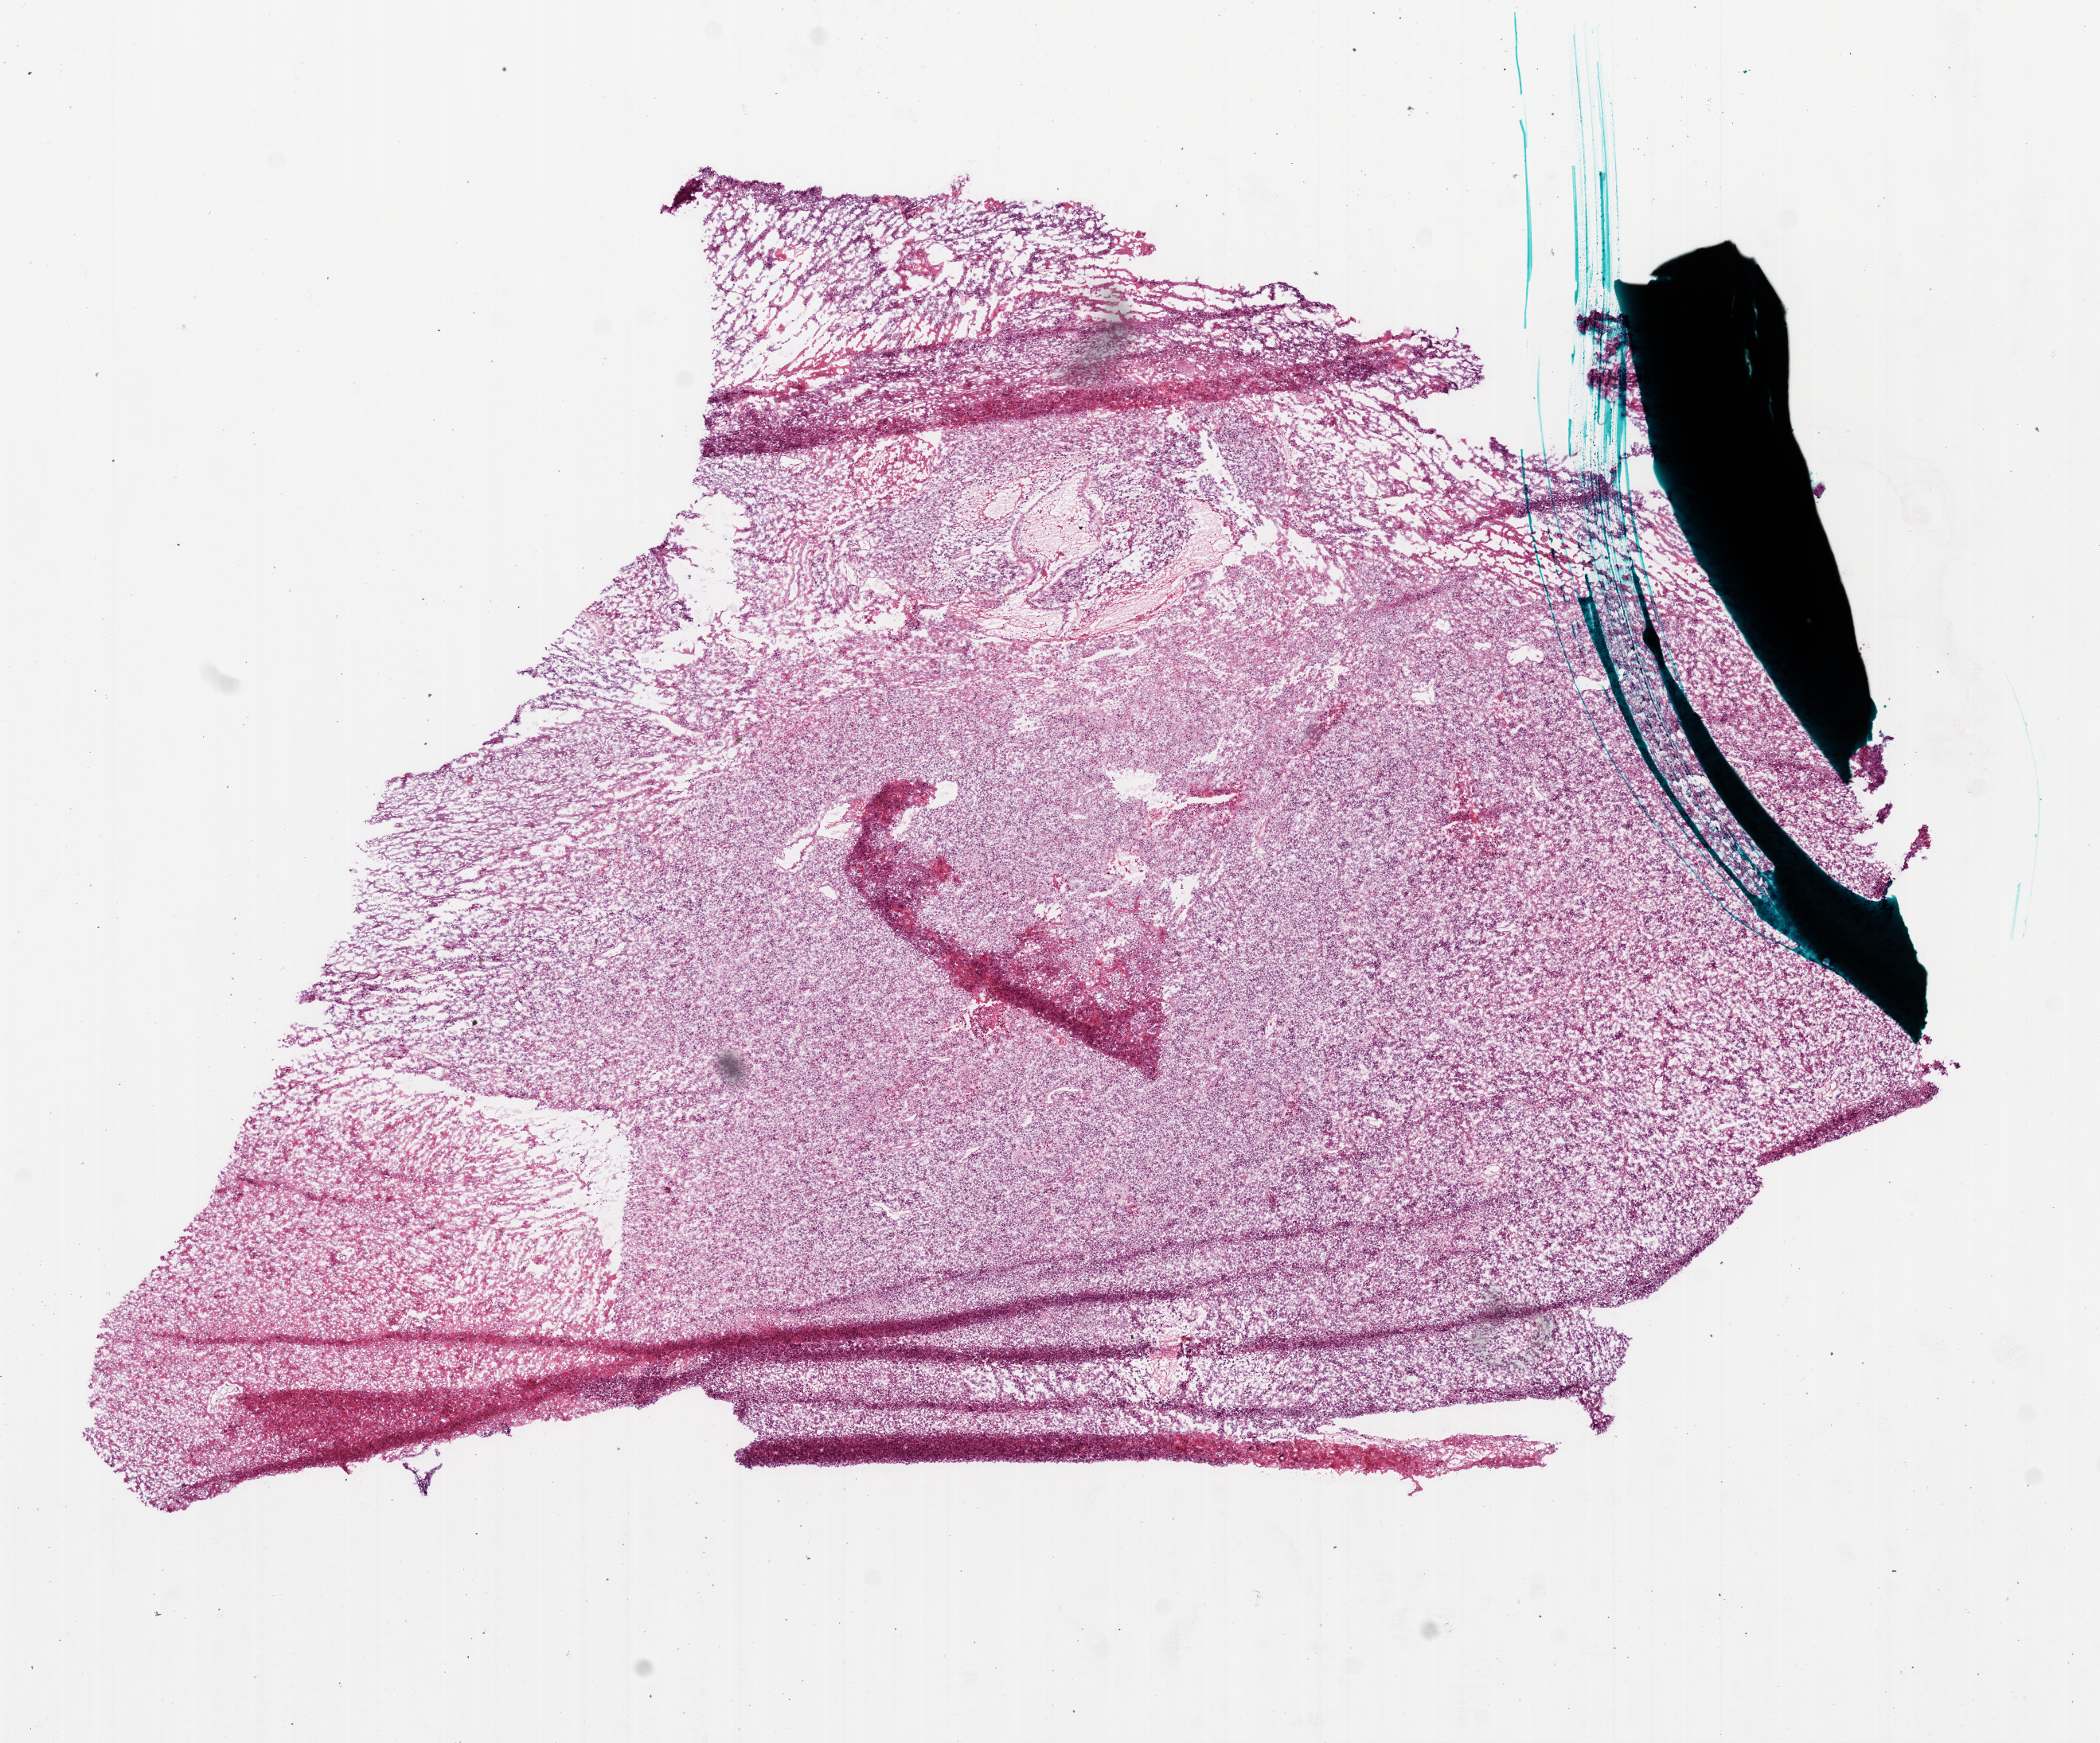
Hematoxylin and eosin (H&E) stained whole-slide image, a low-resolution overview of the entire scanned area, about 10.6 x 8.8 mm. Frozen section from the bottom of the tissue portion. Sample: primary tumour, brain. Patient: female, age at initial diagnosis 61 years.
Diagnosis: Glioblastoma.